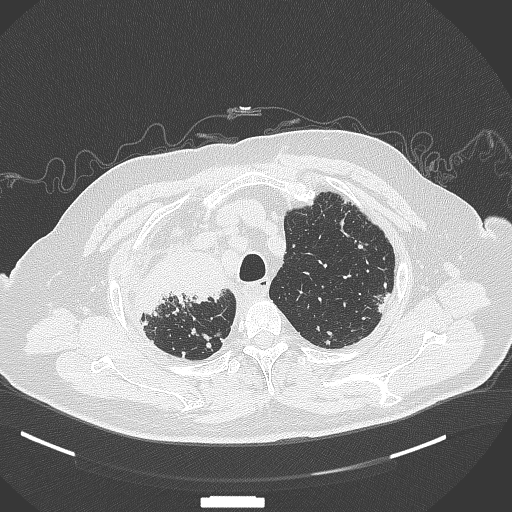
Chest CT, one axial slice. Position 300 of 384 along the scan axis. Lung window (W 1500 / L -600 HU). 1 mm slice thickness. 512 × 512 image matrix, field of view 400 × 400 mm. Patient: male, 69 years. Case-level facts recorded for this patient, not image findings: clinical TNM (as recorded): T4 N3 M1.
Structures marked on this image (rectangle marked by the reading radiologist):
- lung tumour (recorded histology: adenocarcinoma): bounding box <137,252,226,322> (left, top, right, bottom; pixels)